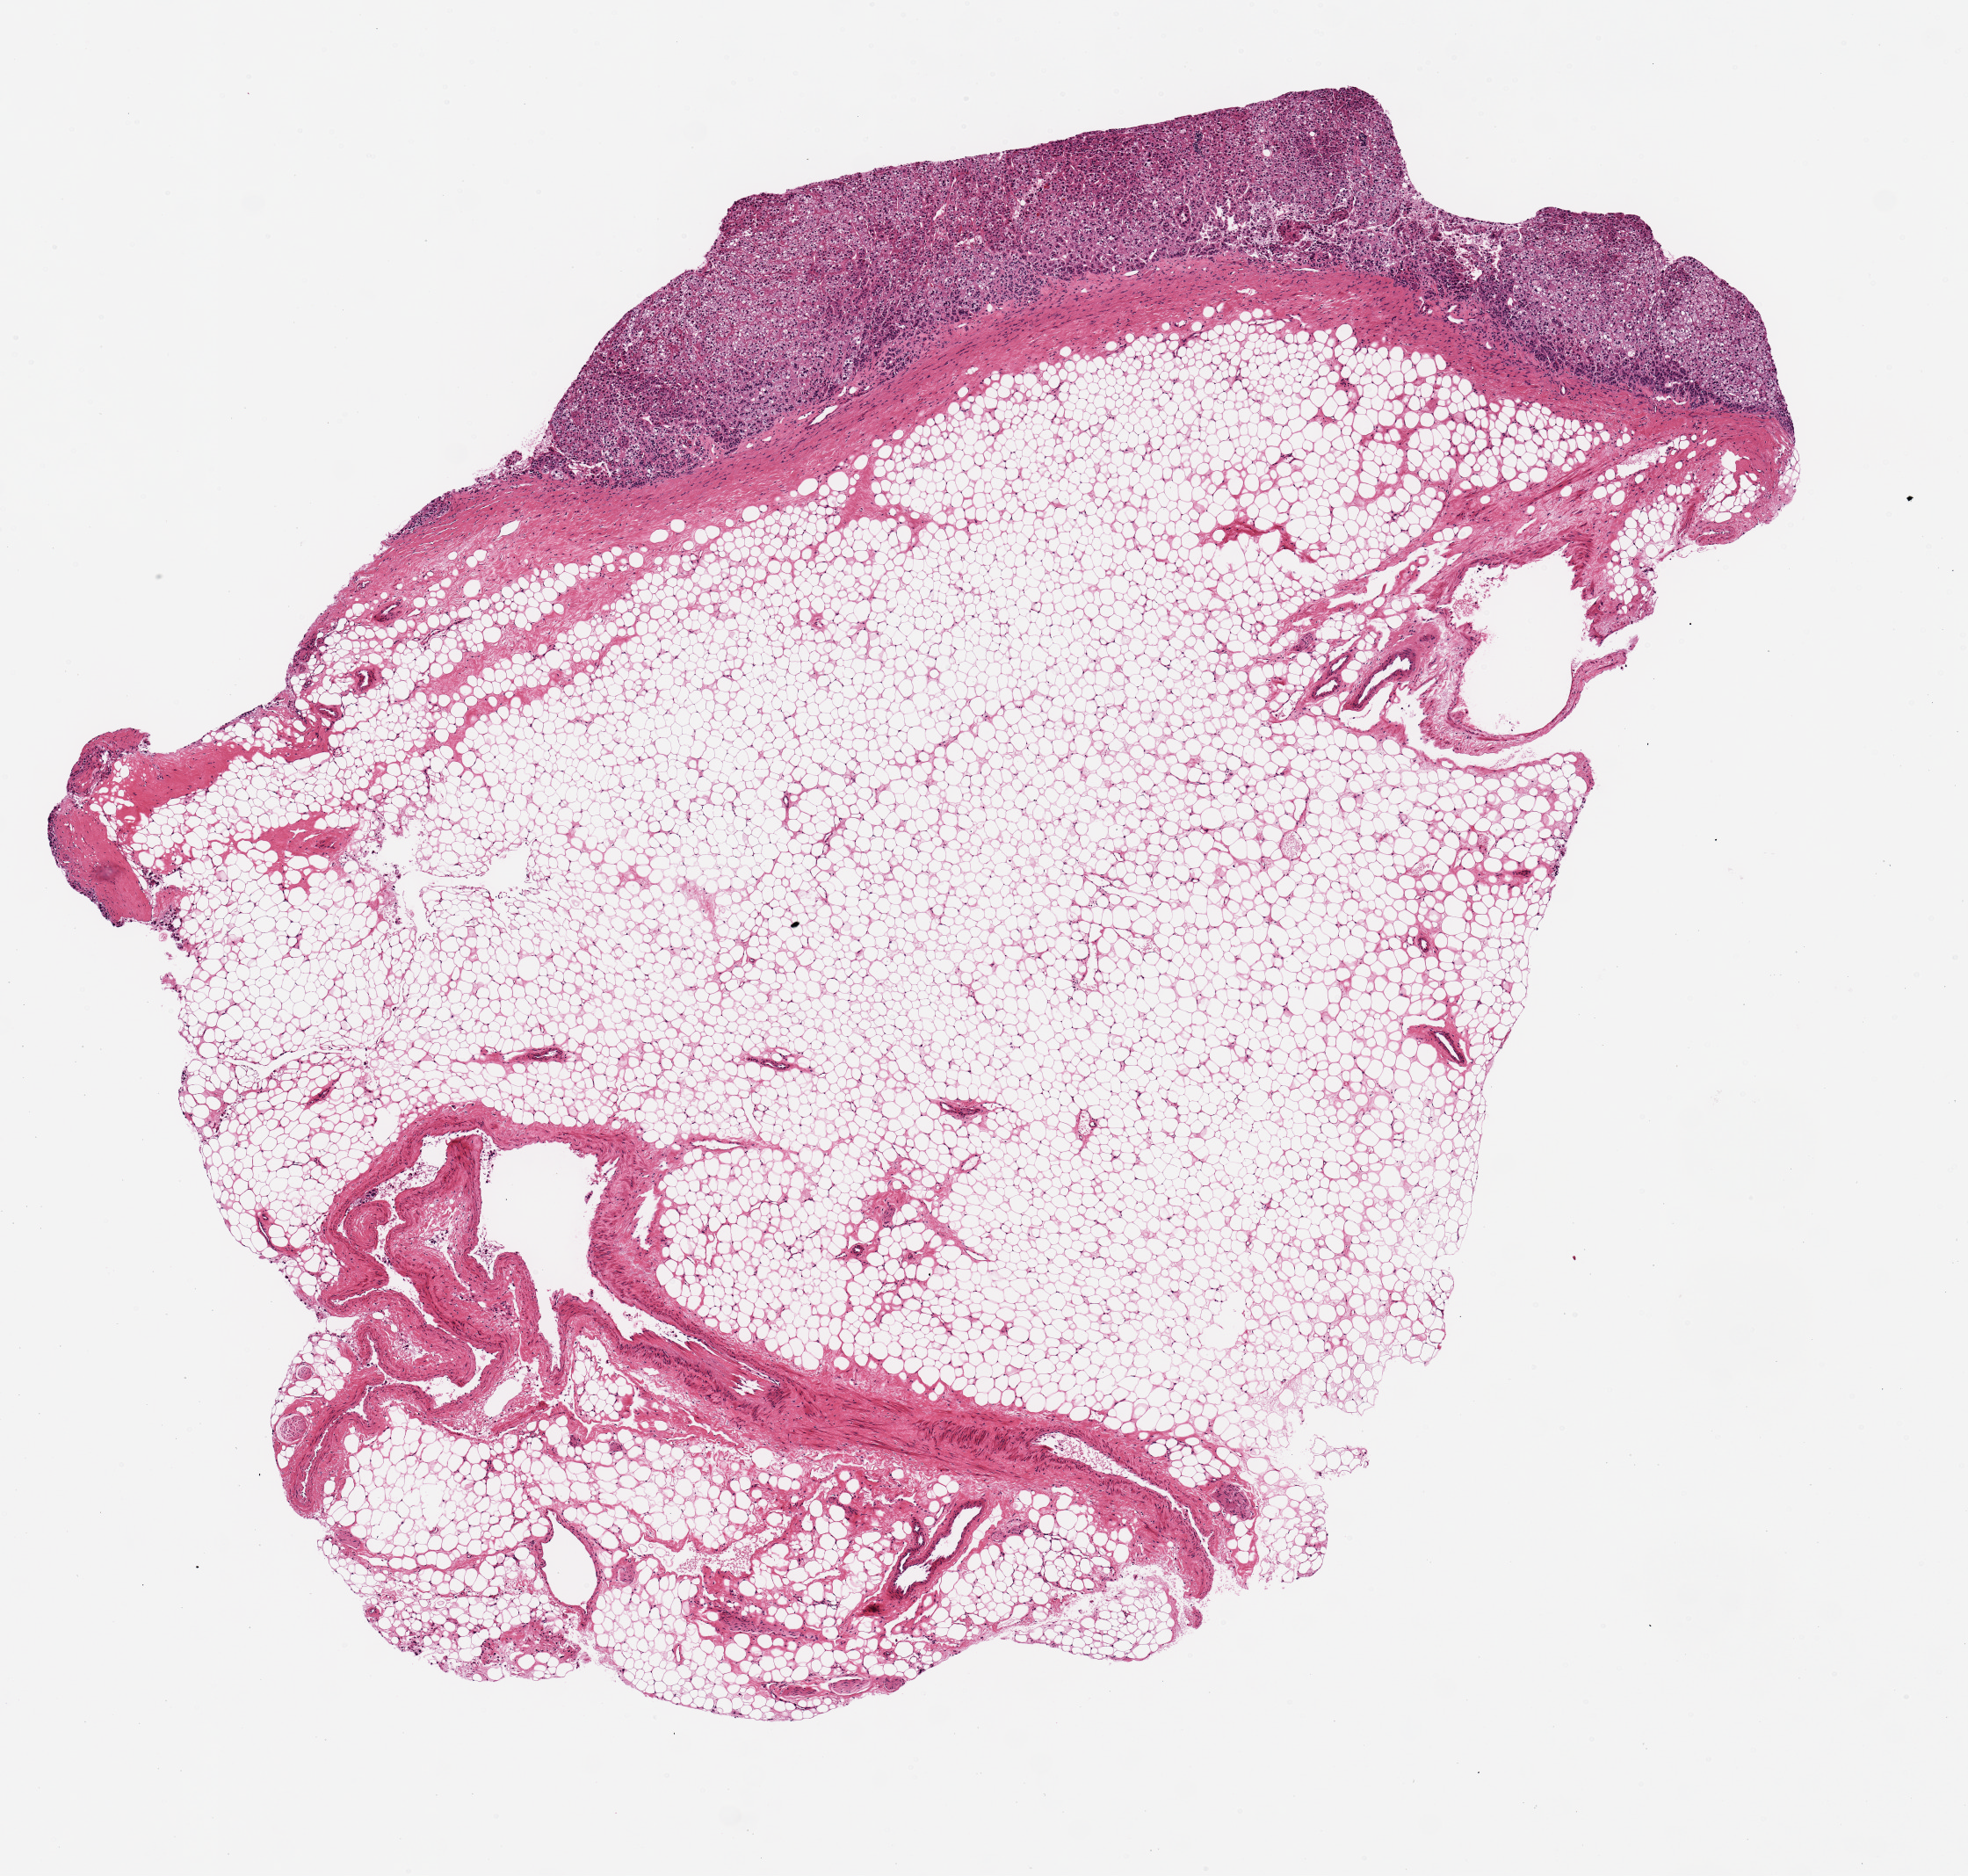
Whole-slide image, hematoxylin and eosin (H&E) stain, a low-resolution overview of the entire scanned area, about 8.9 x 8.4 mm. PAXgene-fixed, paraffin-embedded tissue. Sampled site (target tissue): adrenal gland. Donor tissue sample. Donor sex: male.
Reviewer comment on this tissue sample: Adrenal cortex is l~10% of specimen, a 0.5-1mm fragment on the edge of a 6 x8mm aliquot of fat.